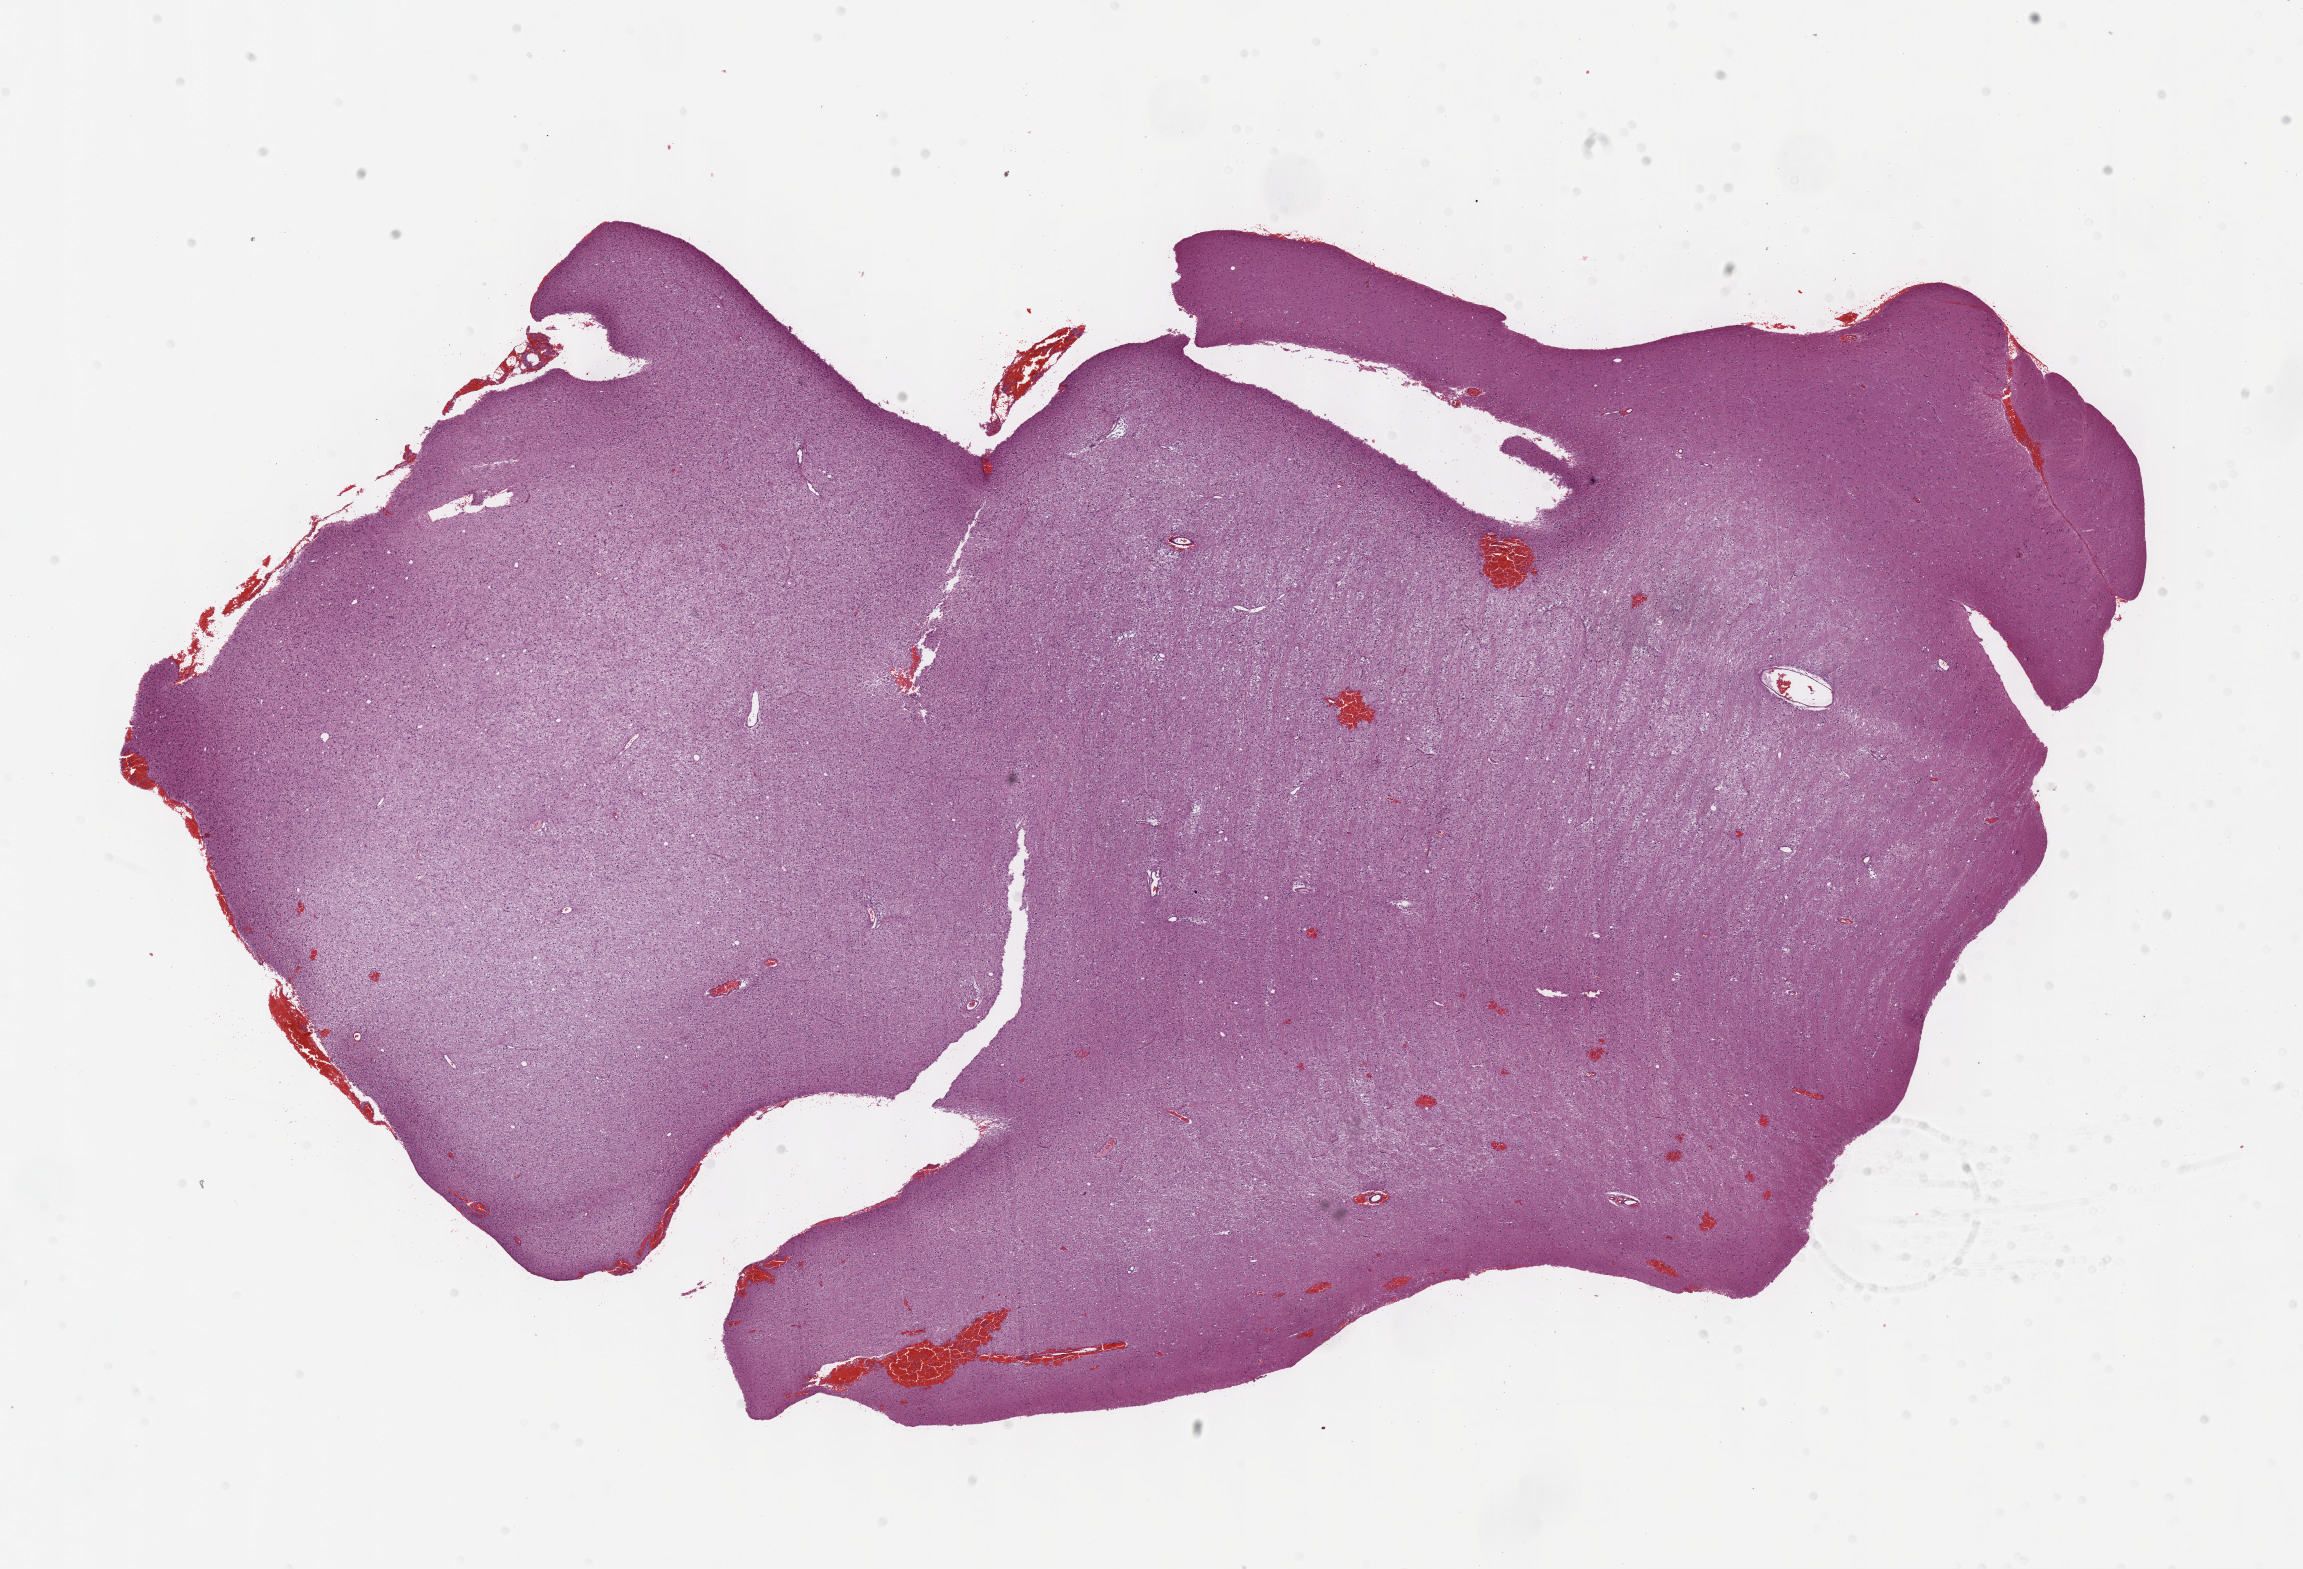
Whole-slide histology image, Hematoxylin and eosin (H&E) stained — a low-resolution overview of the entire scanned area, about 18.6 x 12.7 mm (acquisition: 40x scan). Formalin-fixed paraffin-embedded (FFPE) diagnostic section. Brain, primary tumour sample. Female, age 18 years at initial diagnosis. Histologic grade: G2 (moderately differentiated).
* laterality: left
* diagnosis: Mixed glioma